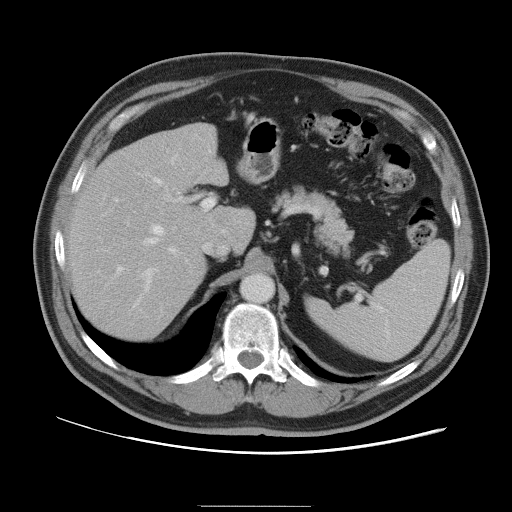
Contrast-enhanced abdominal CT, one axial slice. Slice 67 of 105 in the series (ordered by position). Intravenous contrast given. Soft-tissue window (W 400 / L 40 HU). 5 mm slice thickness. 512 × 512 image matrix. Male patient, age 64 years. Case-level facts recorded for this patient, not image findings: diagnosis: colorectal cancer liver metastases, imaged before liver resection; multiple liver metastases: yes; largest metastasis: 3 cm; disease in both lobes: yes.
Outlined on this slice (outlined manually by an expert reader):
- hepatic veins: box from (x=145, y=162) to (x=173, y=281) px
- liver: (x=68, y=124)–(x=255, y=341)
- planned liver remnant (the part of the liver to remain after resection): (x=68, y=138)–(x=255, y=342)
- portal vein (with intrahepatic branches): (x=115, y=196)–(x=215, y=274)